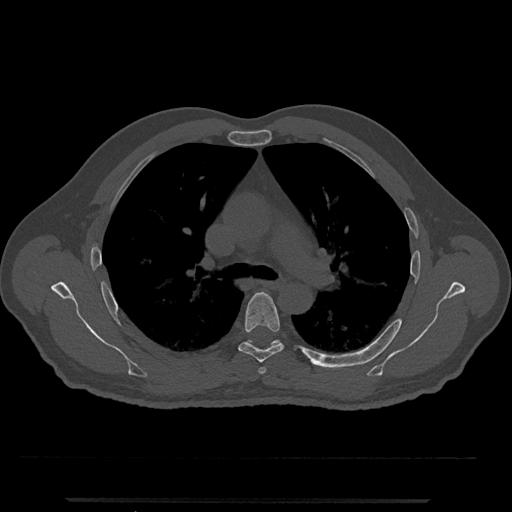
CT including the spine, one axial slice. Position 787 of 797 along the scan axis. Reconstruction kernel Br40s/3. Bone window (W 1800 / L 400 HU). 0.5 mm slice thickness. 512 × 512 image matrix, field of view 419 × 419 mm. Patient: male, 63 years. Case-level facts recorded for this patient, not image findings: primary cancer: prostate.
Annotated regions visible in this slice (semi-automatically segmented with operator editing):
- T5 vertebra: bounding box (x1, y1, x2, y2) in pixels: (238, 292, 284, 363)
- T6 vertebra: (248, 340, 281, 346)